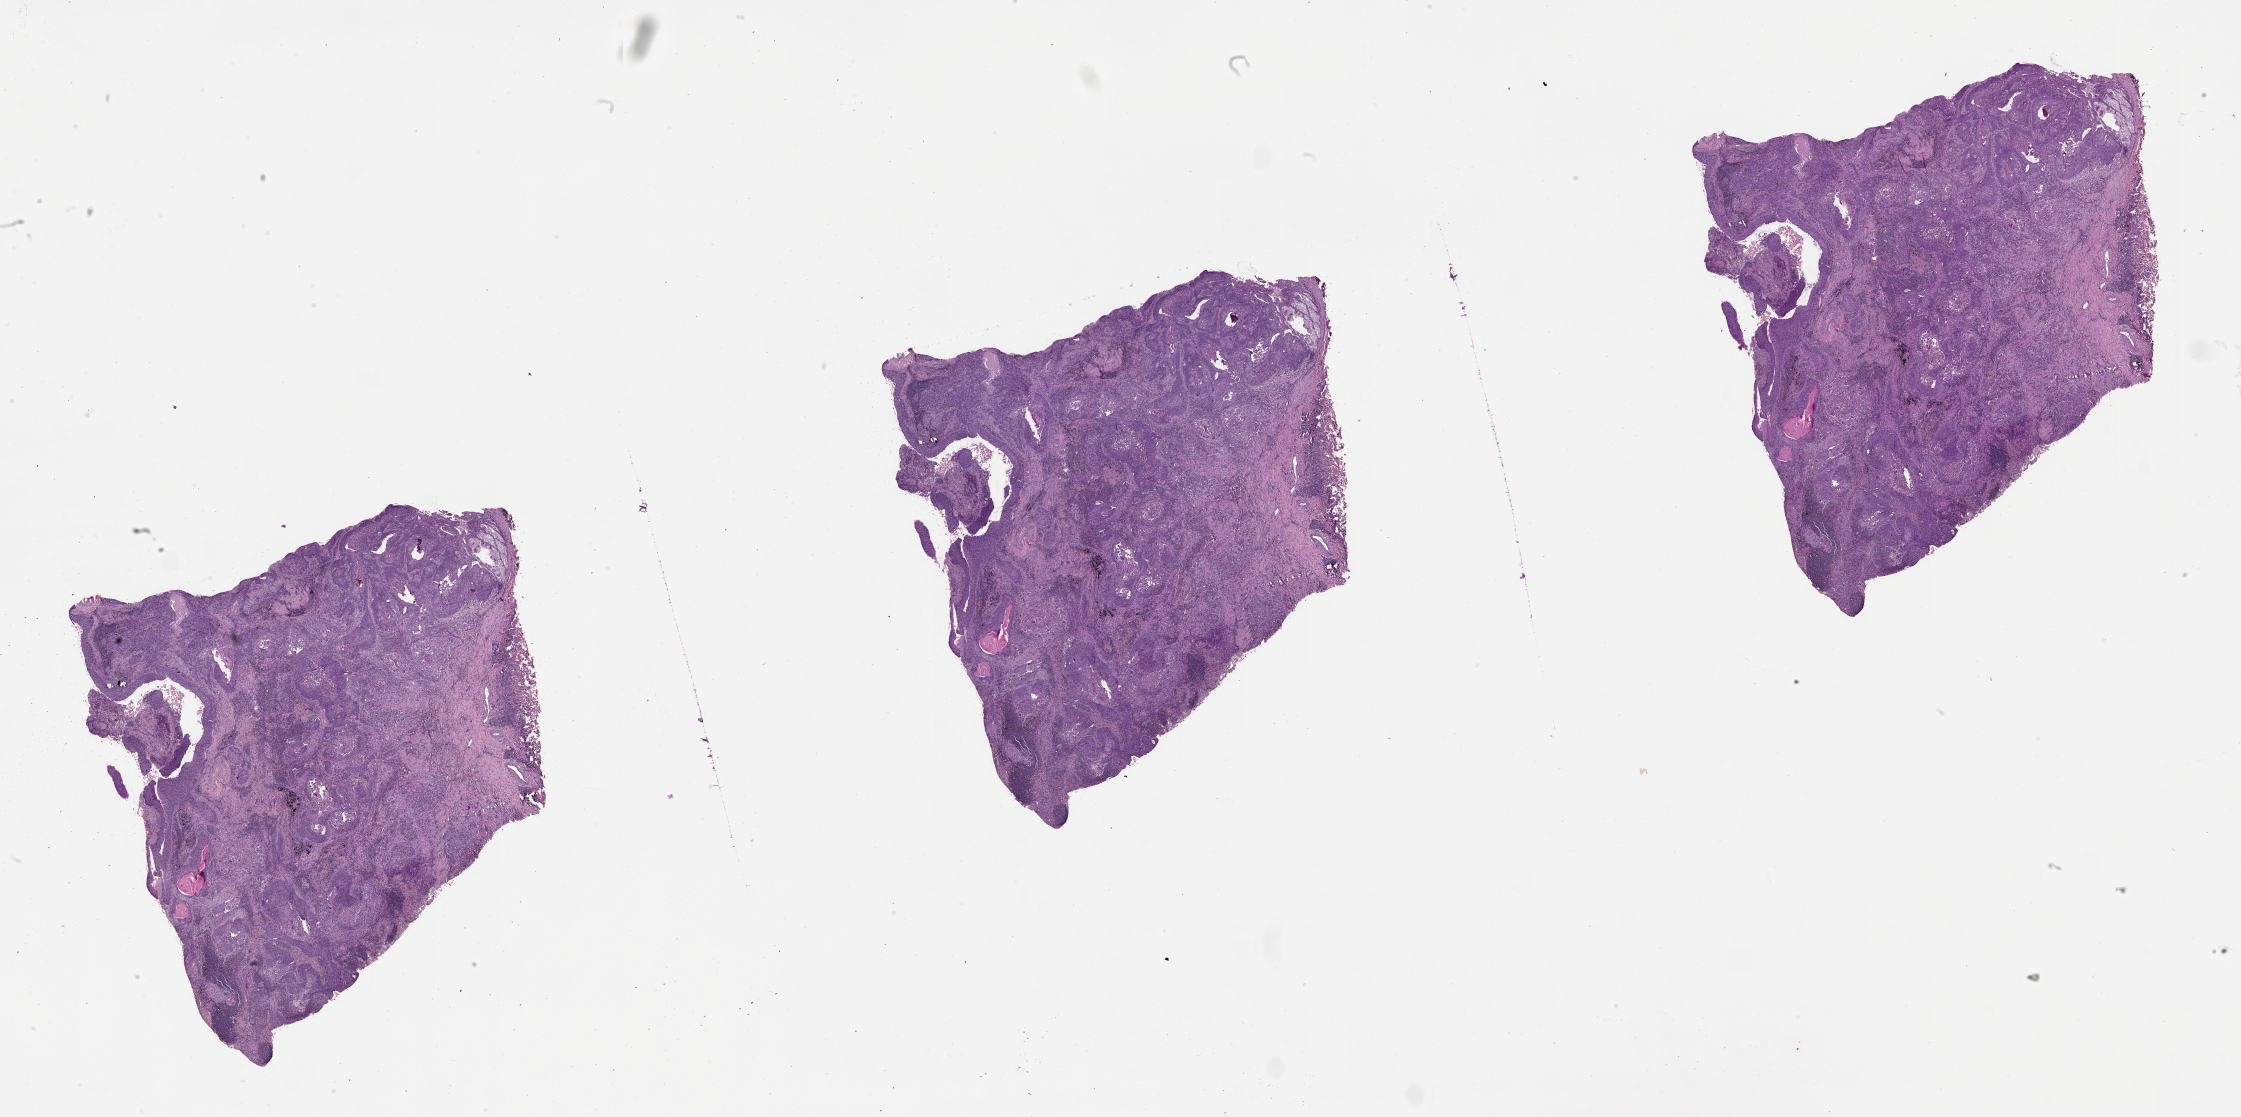
Hematoxylin and eosin (H&E) stained whole-slide image — a low-resolution overview of the entire scanned area, about 36.1 x 18.0 mm (from a 20x scan), tumour tissue sample, lung. Male, 67 y/o.
• patient diagnosis (cohort enrolment): squamous cell carcinoma (lung)